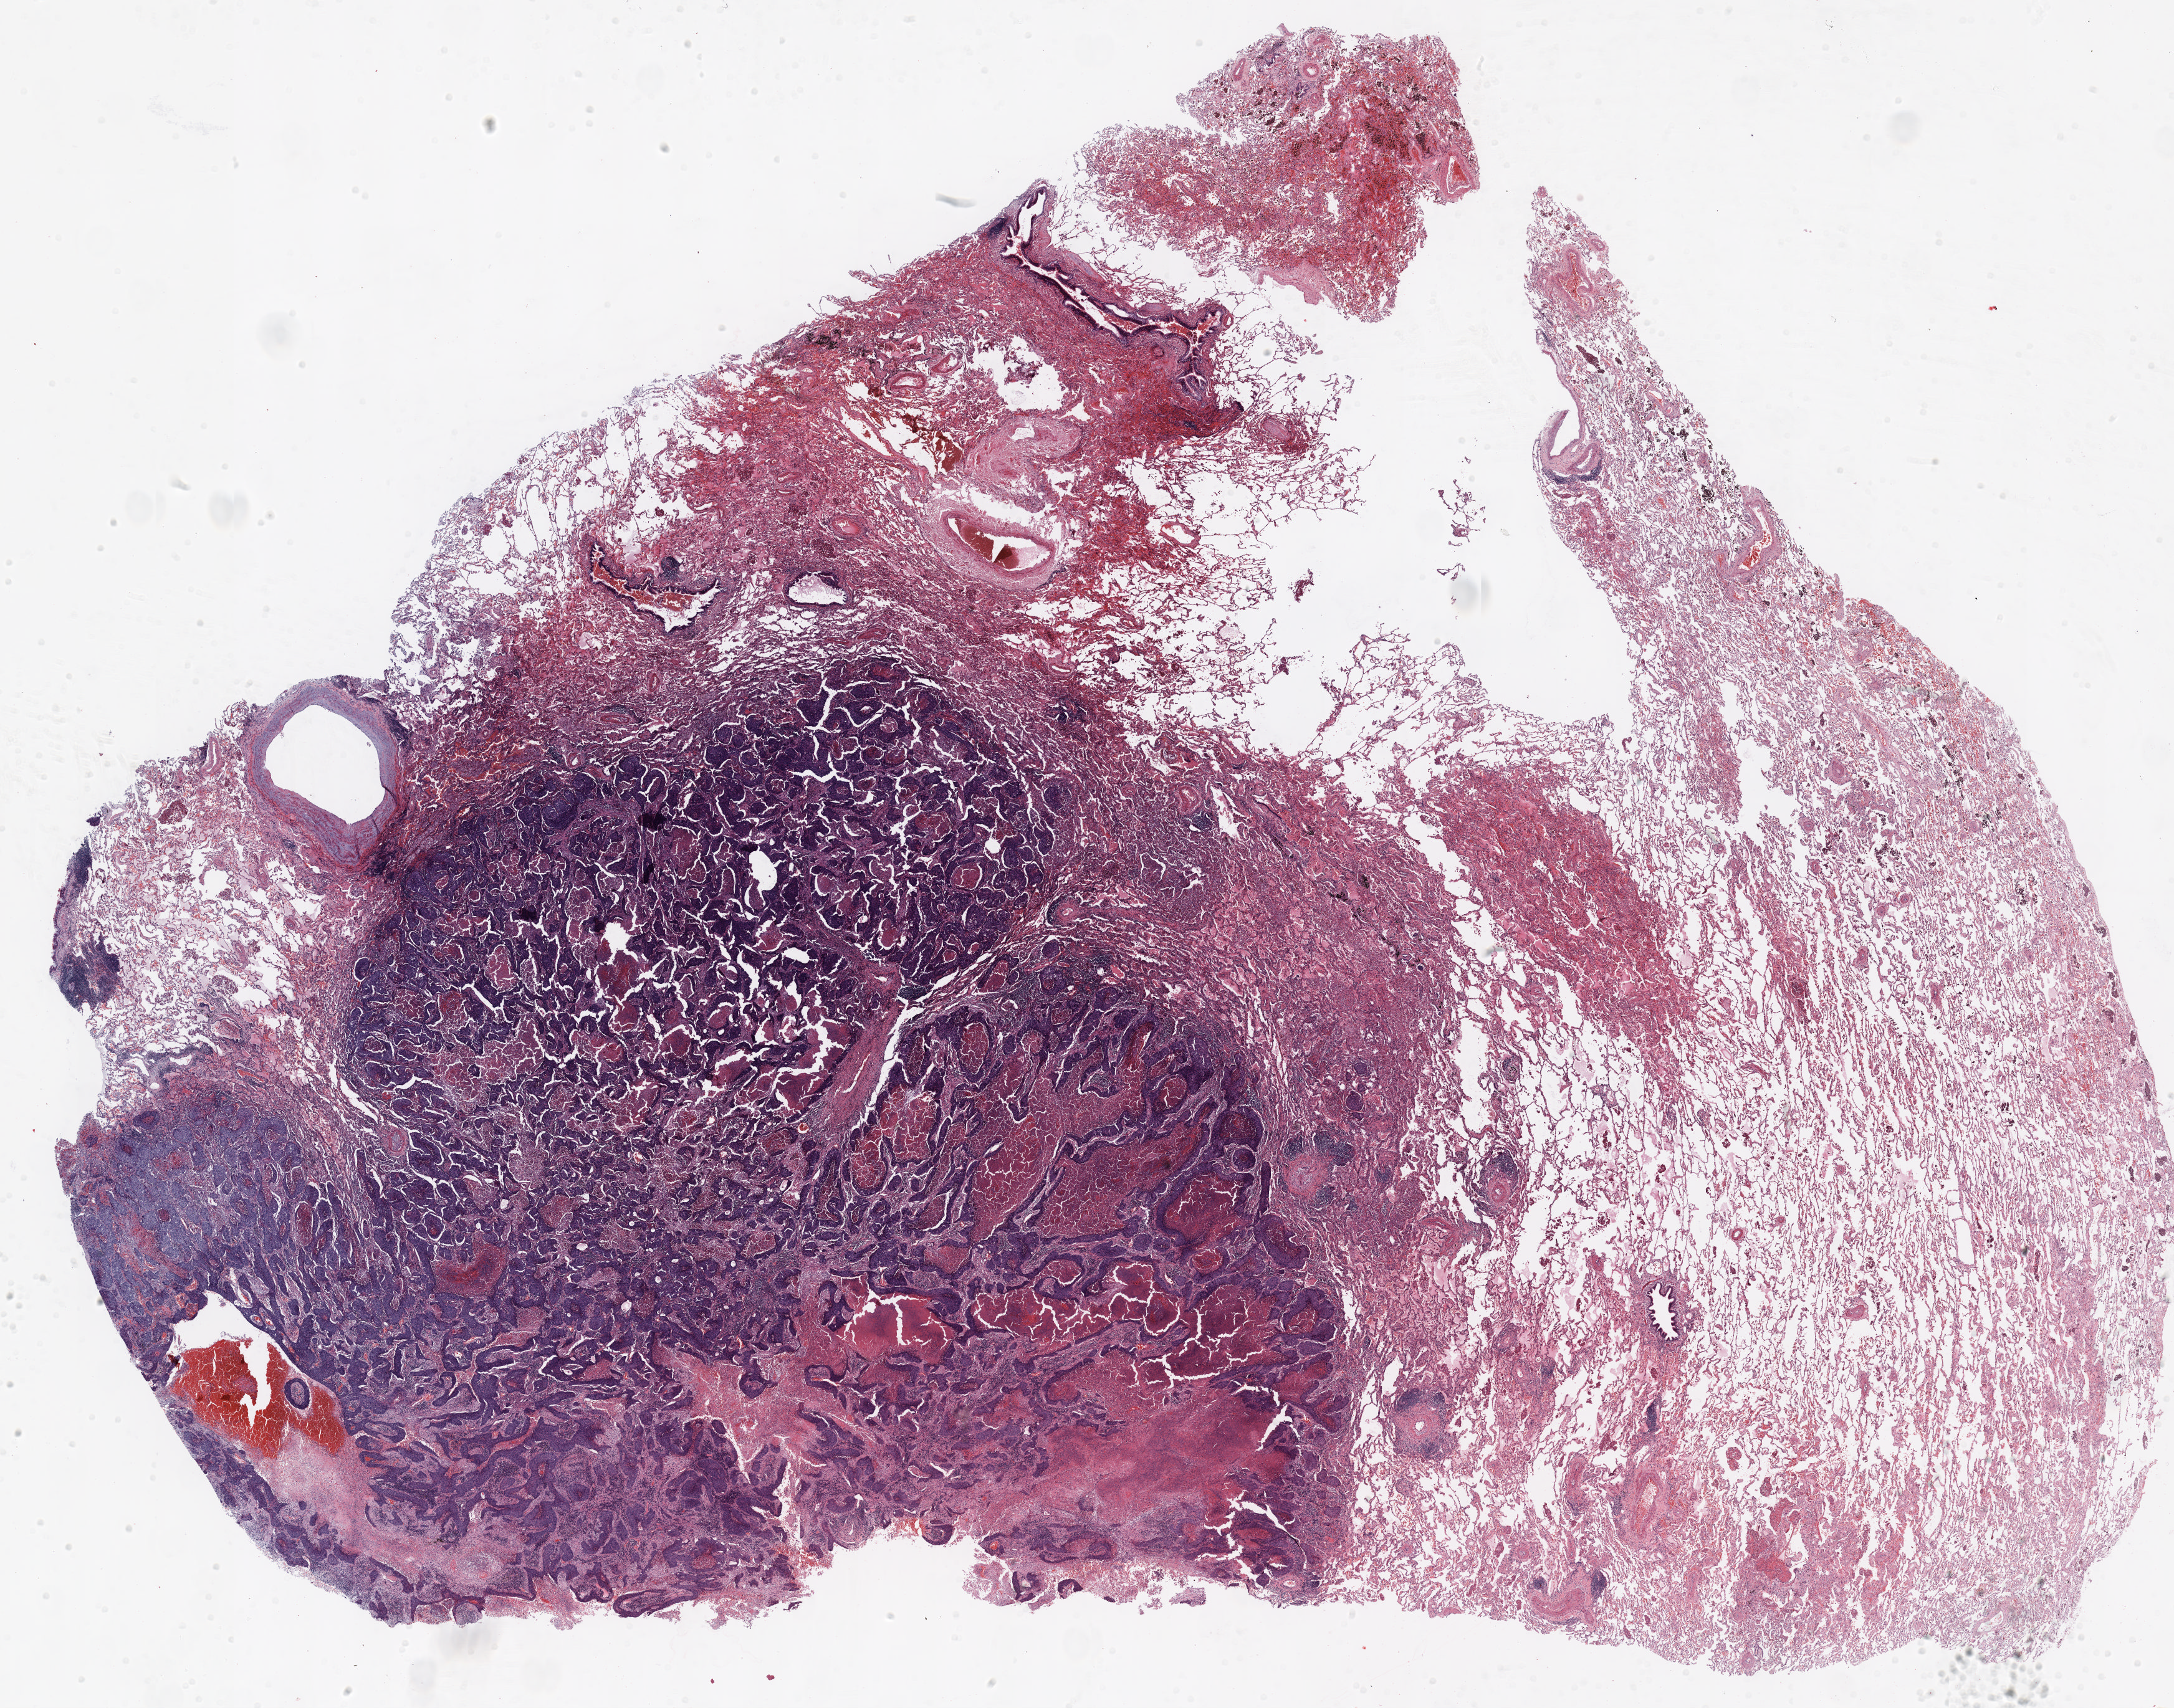
Hematoxylin and eosin (H&E) stained whole-slide image, whole scanned area (about 28.0 x 22.0 mm) shown as a low-resolution overview, FFPE section, lung. Female patient, aged 58 at enrolment. Current smoker at enrolment. Grade: poorly differentiated (G3).
Stage (AJCC 6th edition): IA. Primary tumour location (clinical record): right lower lobe. Participant's lung-cancer diagnosis: Non-small cell carcinoma (ICD-O-3 8046/3). Tumour size (pathology): 25 mm. ICD-O-3 topography: lower lobe of lung (C34.3).